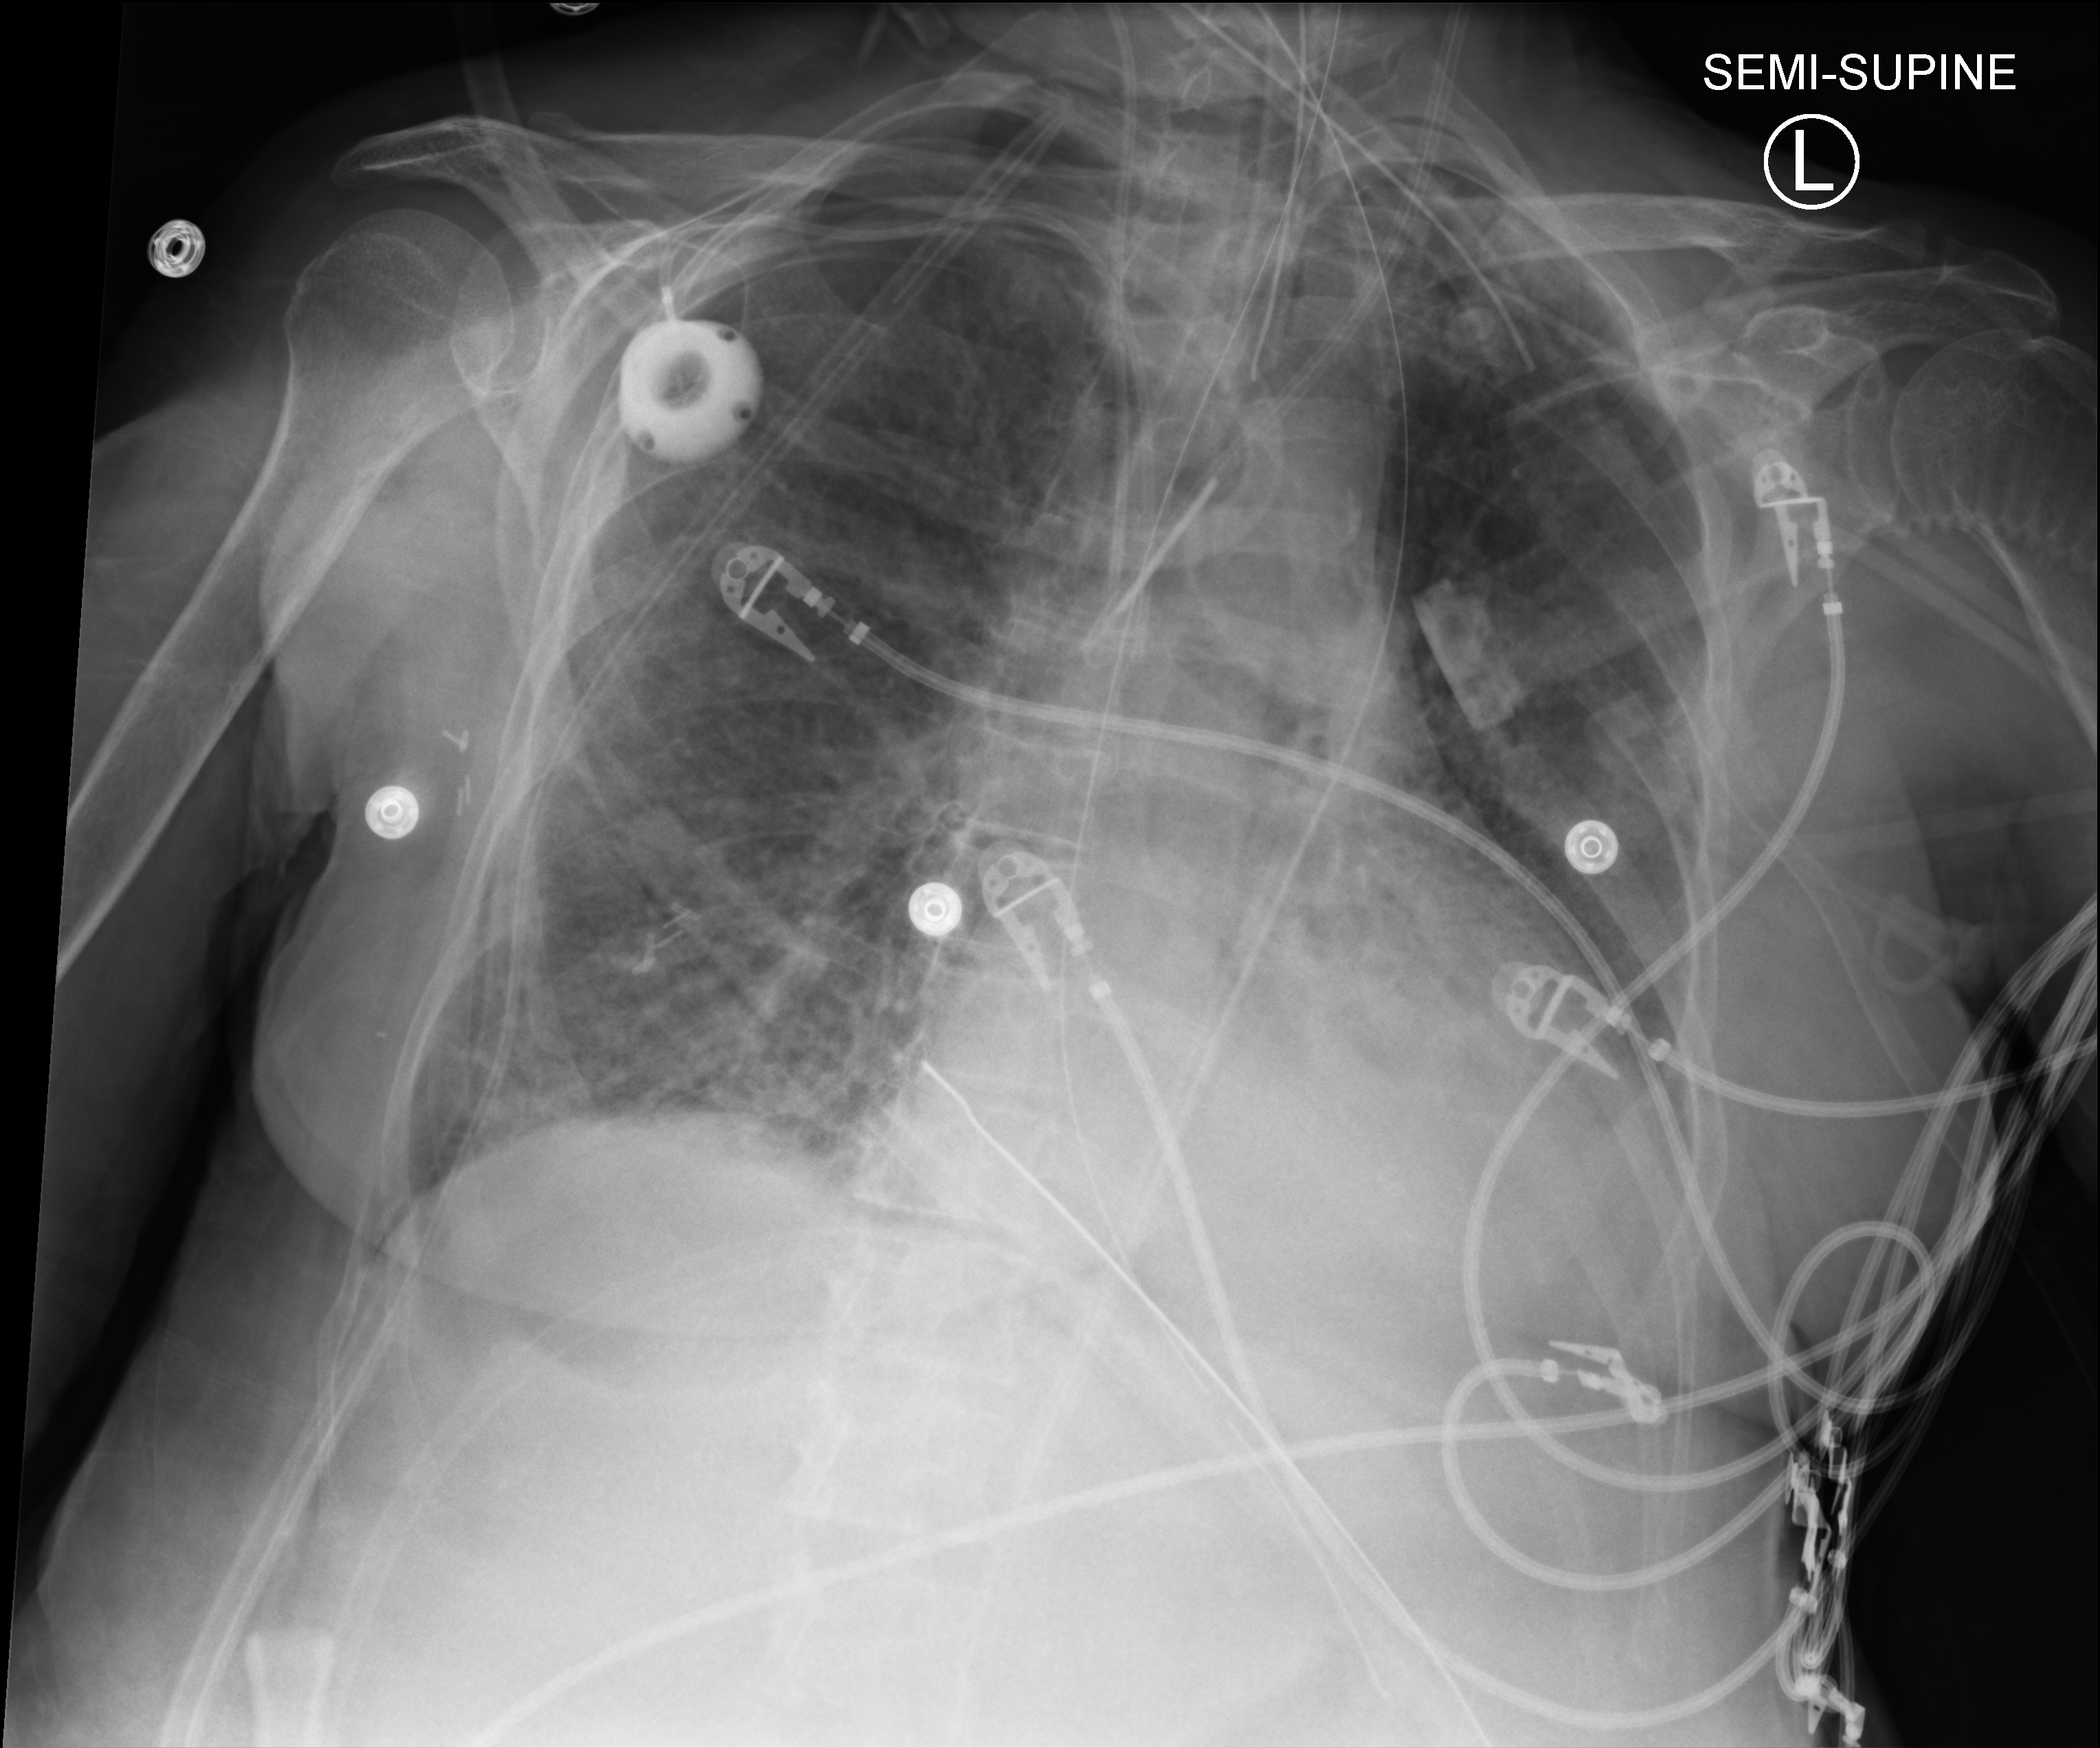
Portable chest radiograph; anteroposterior (AP) projection. Female patient hospitalised with COVID-19, age 60–74 years.
Hospital-stay facts (about this admission, not read from this image; timing relative to this image not recorded):
- COPD (admission record): no
- mechanically ventilated during this hospital stay: yes
- admitted to intensive care during this hospital stay: yes